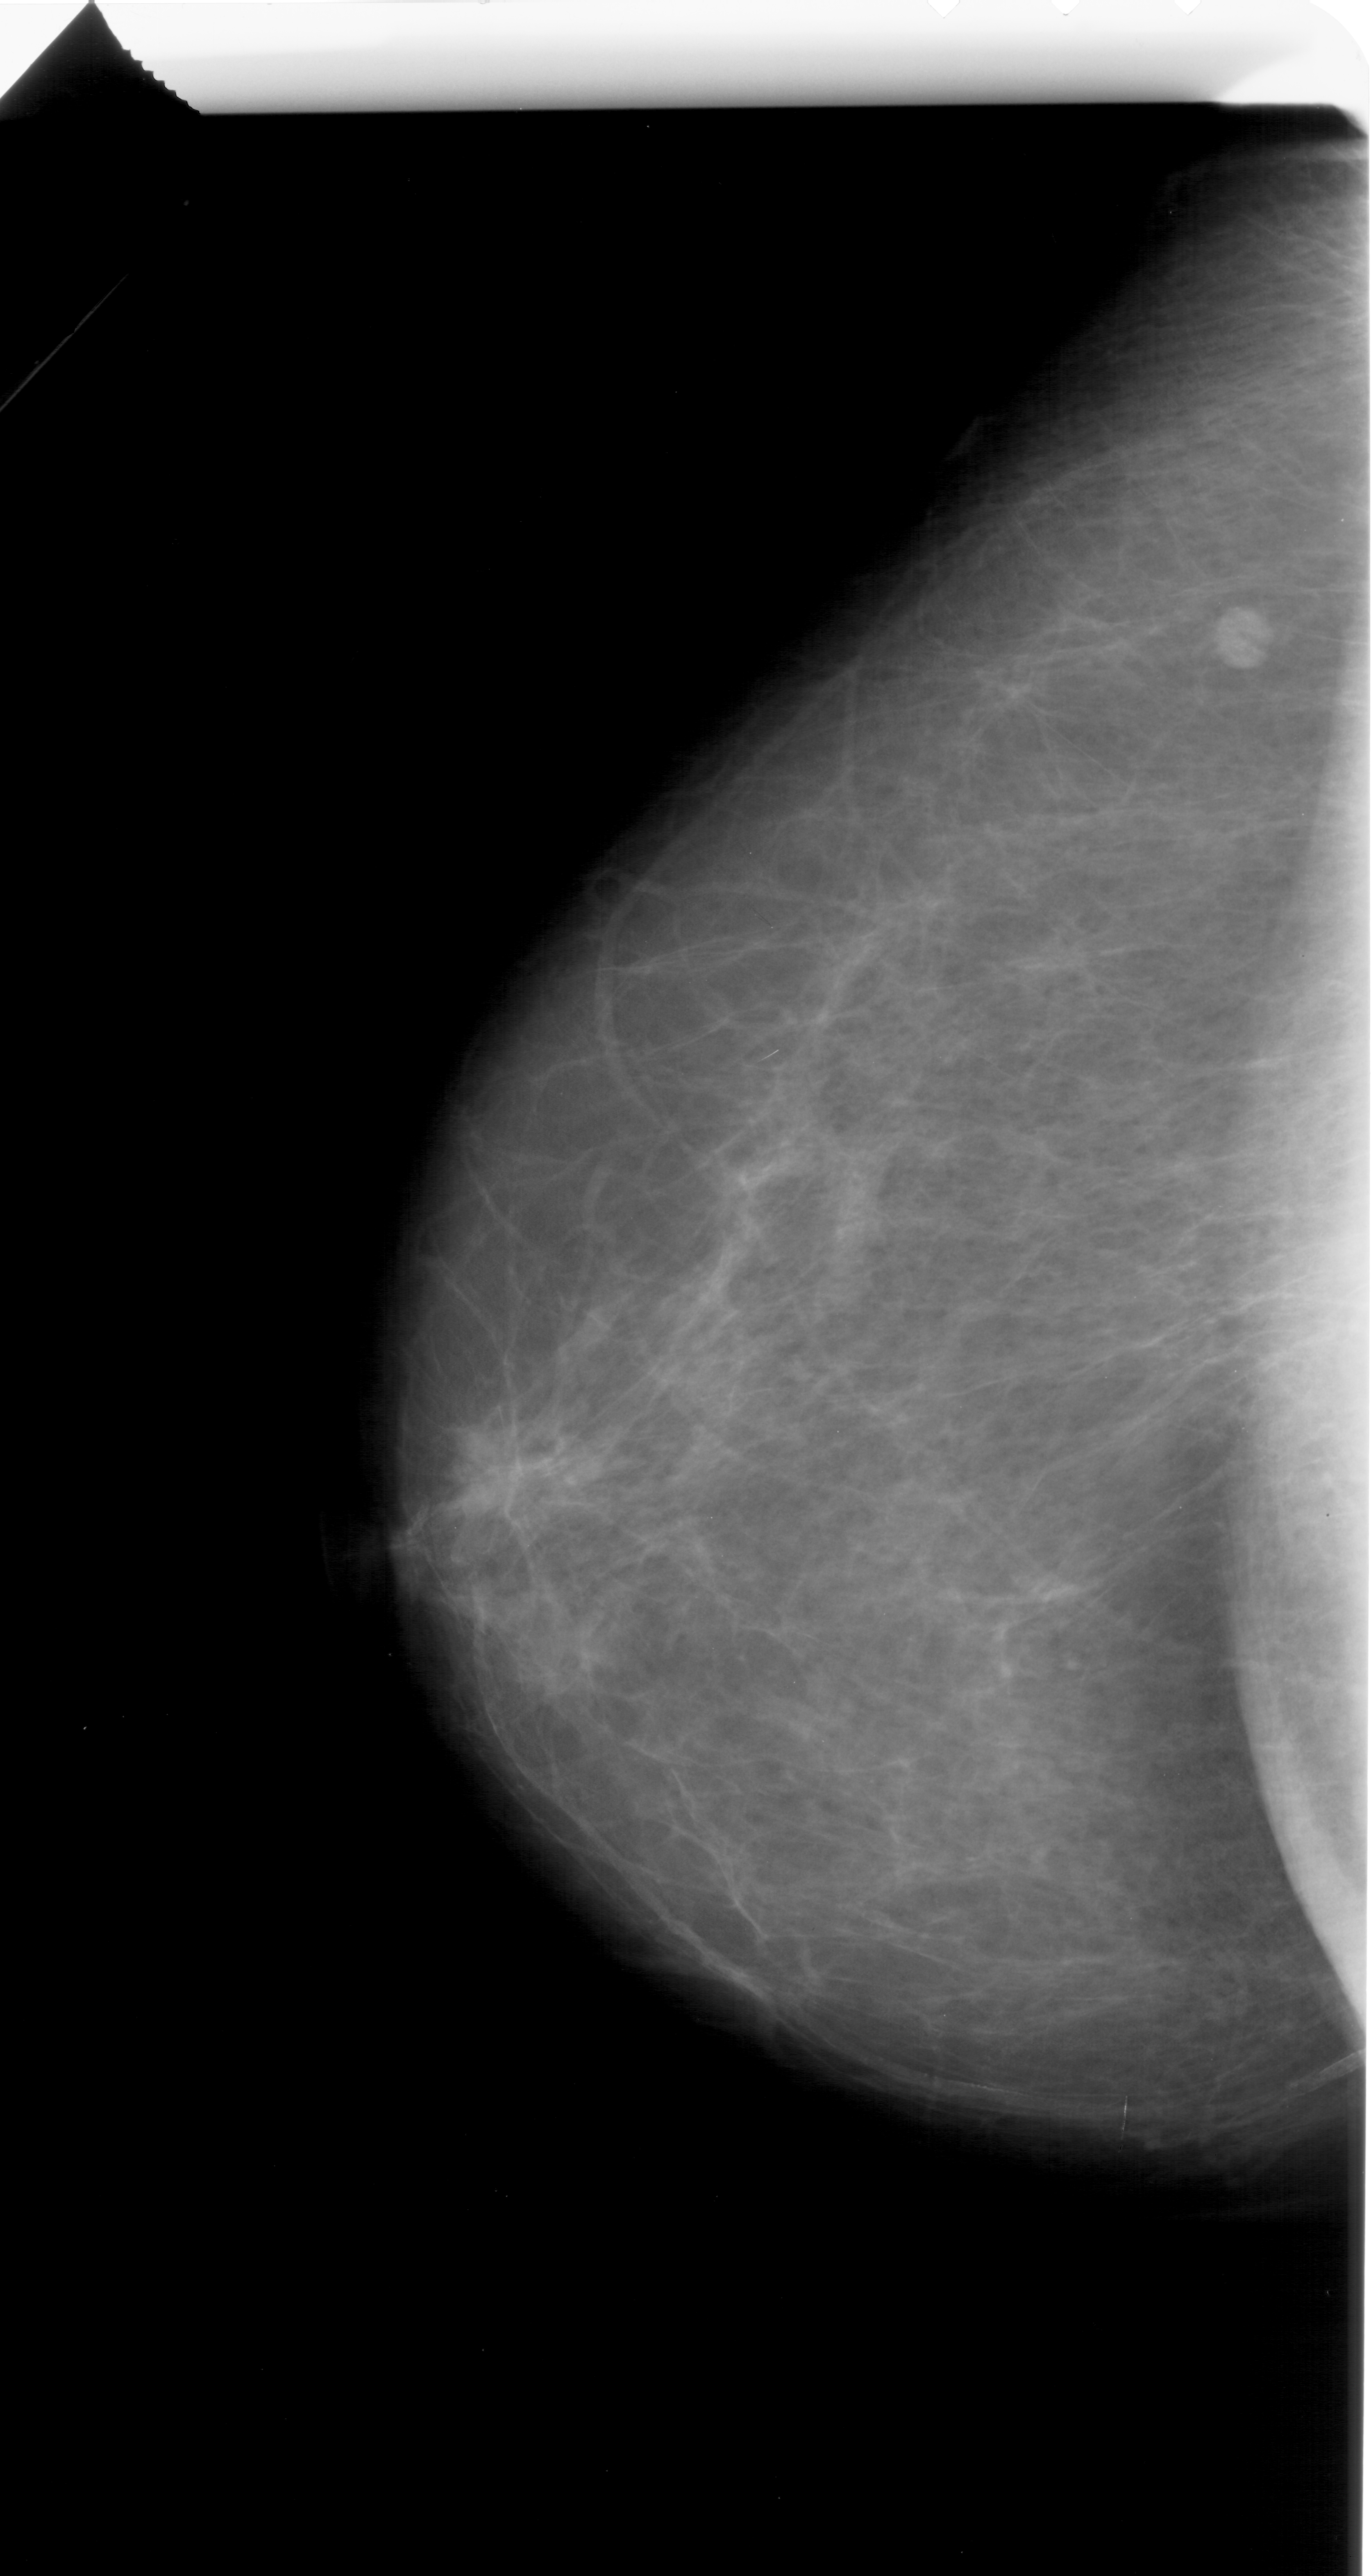
Digitized screen-film mammogram. Left breast. CC view. Breast composition: scattered fibroglandular densities (BI-RADS density category 2 of 4). 1371 × 2576 image matrix.
Expert-marked regions of interest on this image (one box per marked abnormality):
- mass, shape irregular, margins spiculated; BI-RADS assessment category 5; subtlety rating 1 on a 1 (subtle) to 5 (obvious) scale; pathology (as recorded): malignant: bounding box [x1, y1, x2, y2] px = [447, 1404, 571, 1536]